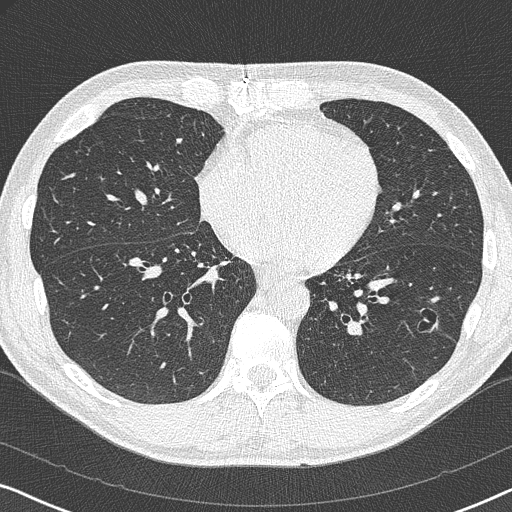
Low-dose screening chest CT, axial slice, first (baseline) screen, lung window (W 1500 / L -600 HU). Male participant, aged 59 years at enrolment. Current smoker at enrolment.
- Expert reader's lesion annotation, bounding box <411,303,450,338> (left, top, right, bottom; pixels).
- The screening reader recorded 2 non-calcified nodules or masses ≥4 mm on this exam (left lower lobe, right middle lobe); which of them this box marks is not recorded.
- Official screen result: positive, change unspecified: nodule(s) >= 4 mm or enlarging nodule(s), mass(es), or other non-specific abnormalities suspicious for lung cancer.
- Lung cancer was diagnosed 821 days after this screen: adenocarcinoma, NOS, left lower lobe, poorly differentiated (G3), stage IA (AJCC 6th edition), 20 mm at pathology.